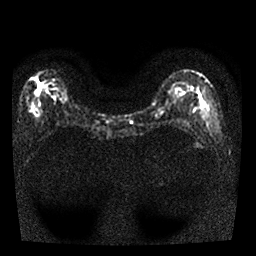
Breast MRI, one axial slice; slice 11 of 25 in the series (ordered by position); diffusion-weighted series; image 2 of 4 stored at this slice position (different b-values; order by instance number); 1.5 T; 4 mm slice thickness; 256 × 256 image matrix, field of view 300 × 300 mm. Female patient.
Outlined on this slice (manually delineated by an expert):
- tumour on diffusion-weighted imaging: box from (x=33, y=76) to (x=46, y=95) px